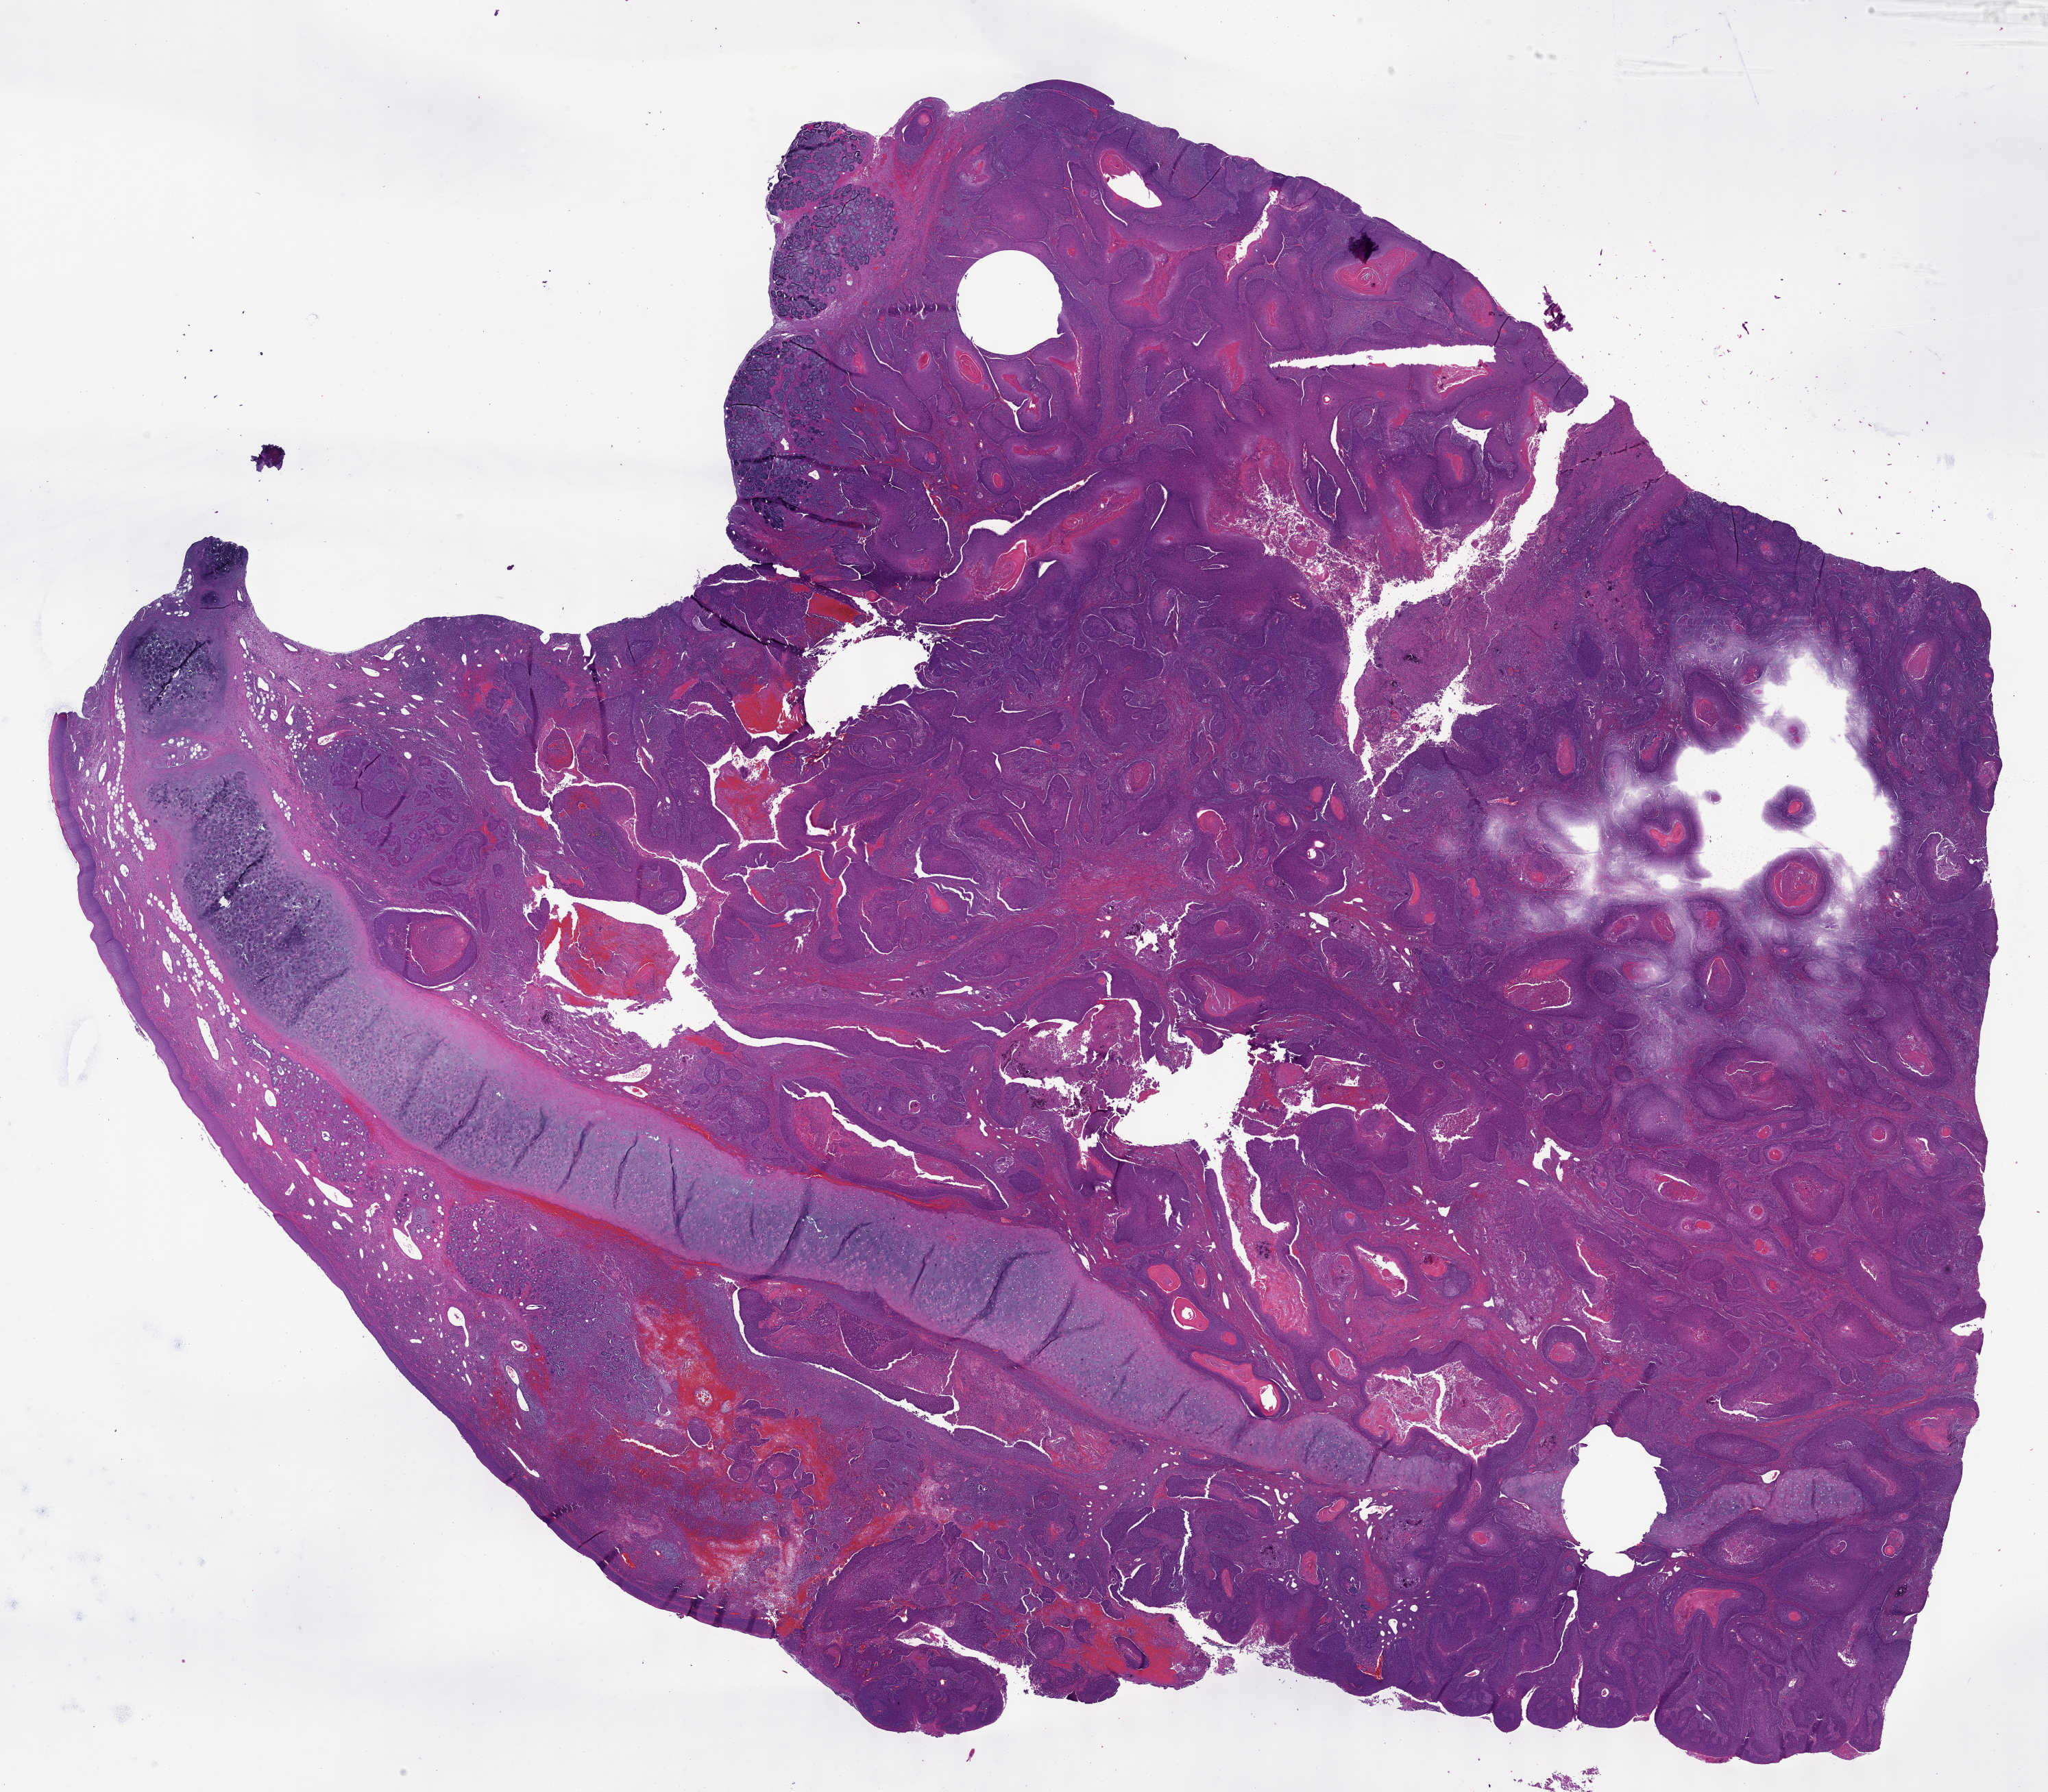
Digitized Hematoxylin and eosin (H&E) stained tissue section (whole slide), shown as a low-resolution overview of the whole scanned area (about 24.1 x 21.1 mm, acquisition: 40x scan), formalin-fixed paraffin-embedded (FFPE) diagnostic section, primary tumour sample from the head and neck. Female, age 53 years at initial diagnosis. Histologic grade: G2 (moderately differentiated).
Diagnosis: Squamous cell carcinoma, NOS (larynx, NOS). AJCC pathologic stage: IVB (7th edition).